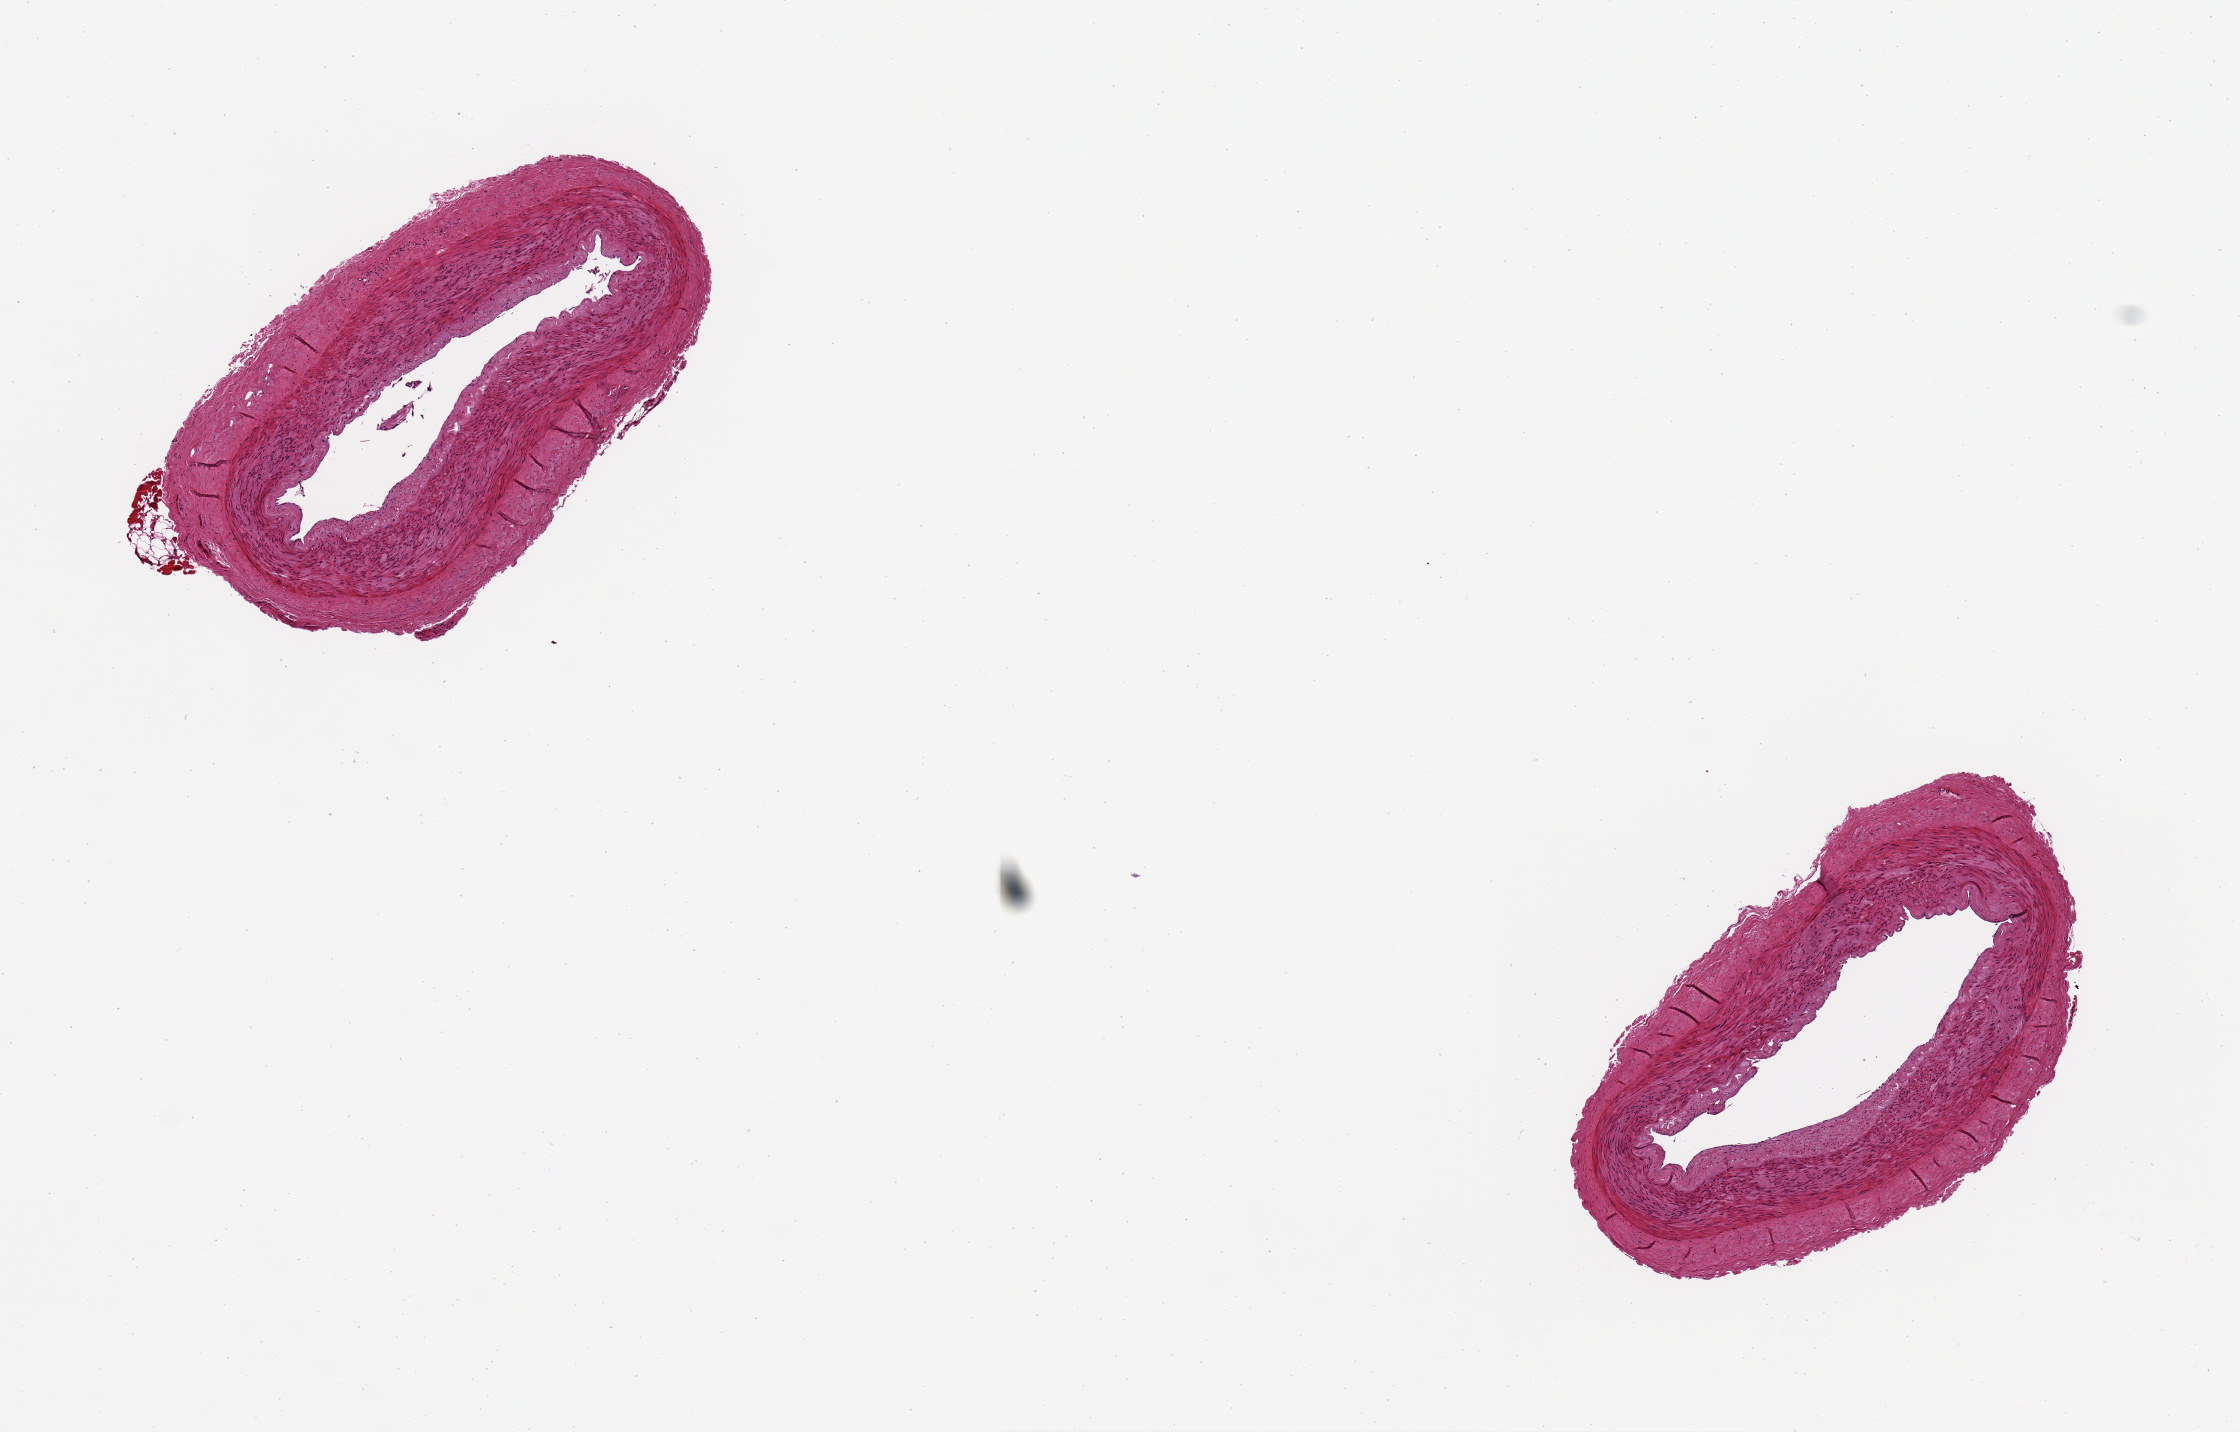
Digitized haematoxylin and eosin-stained section, low-resolution overview of the scanned area, about 8.9 x 5.7 mm. PAXgene-fixed, paraffin-embedded tissue. Sampled site (target tissue): tibial artery. Tissue donor sample. Female donor.
Reviewer comment on this tissue sample: 2 aliquots, ~2.5mm d. Excellent clean specimens.